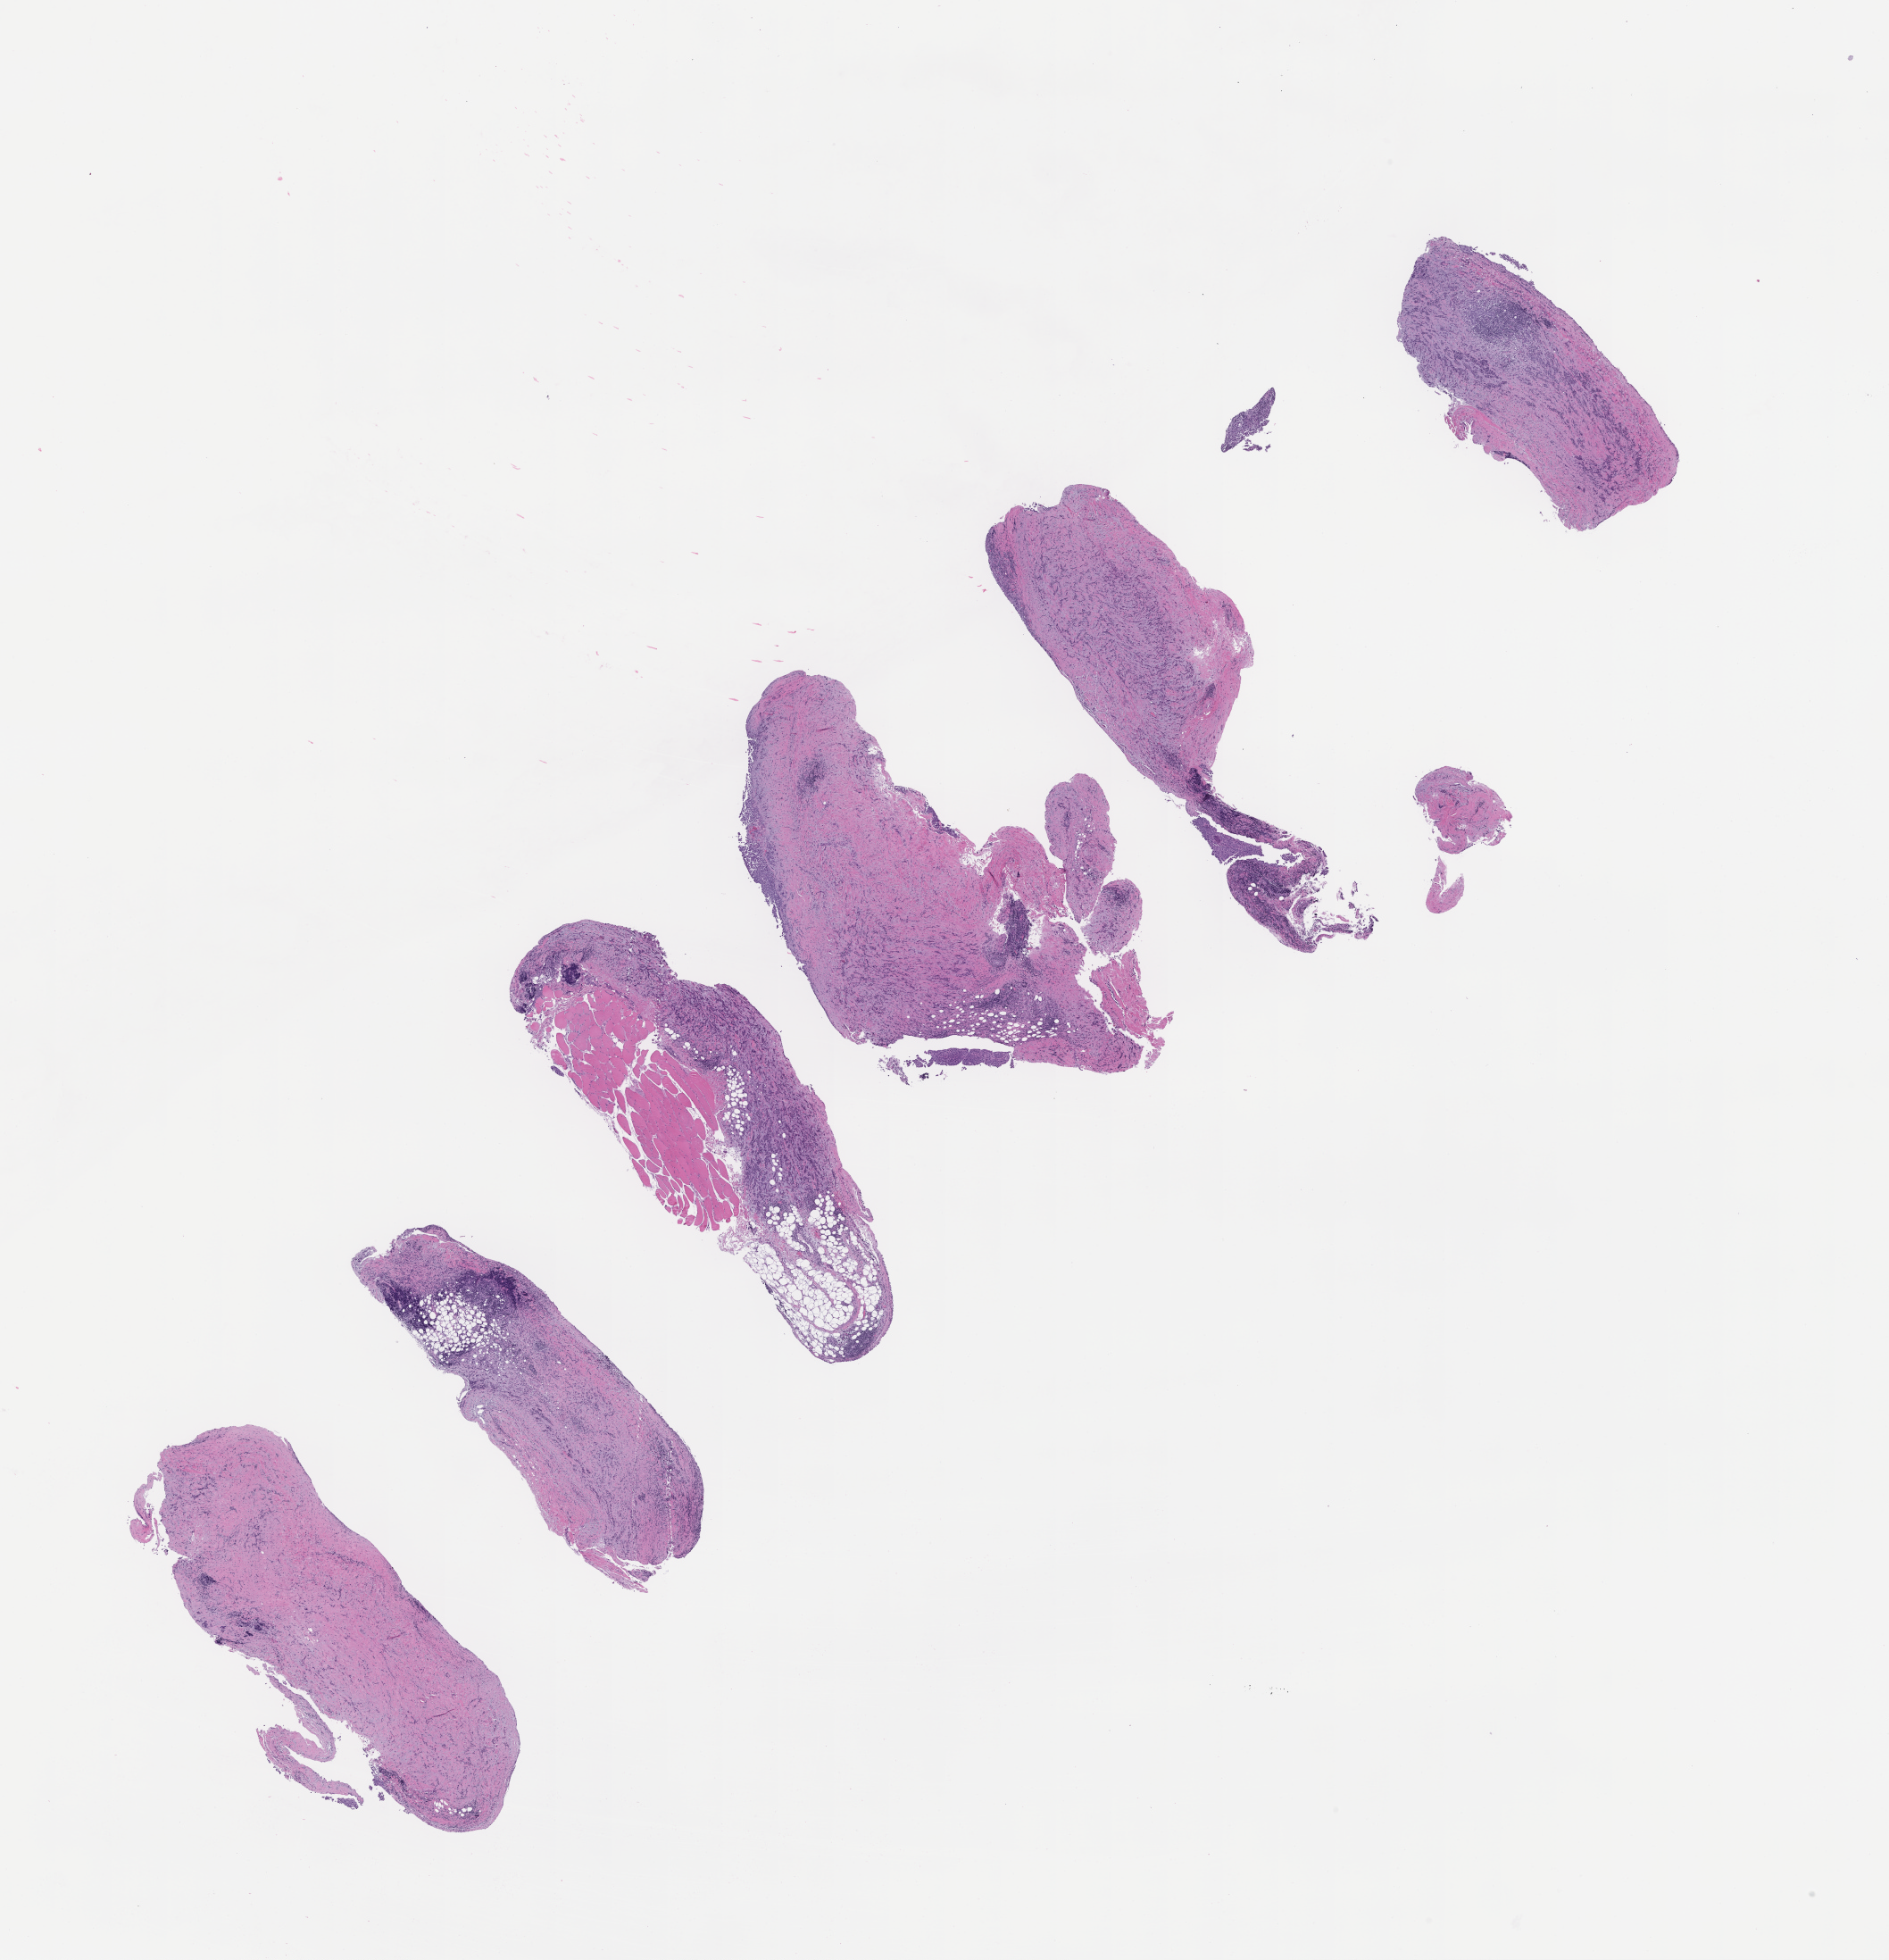
Digitized hematoxylin and eosin (H&E)-stained section, whole scanned area (about 17.1 x 17.7 mm) shown as a low-resolution overview; formalin-fixed paraffin-embedded section; archival tissue. Patient: female.
This section: metastatic tumor tissue. Patient diagnosis (primary): Invasive Breast Carcinoma.